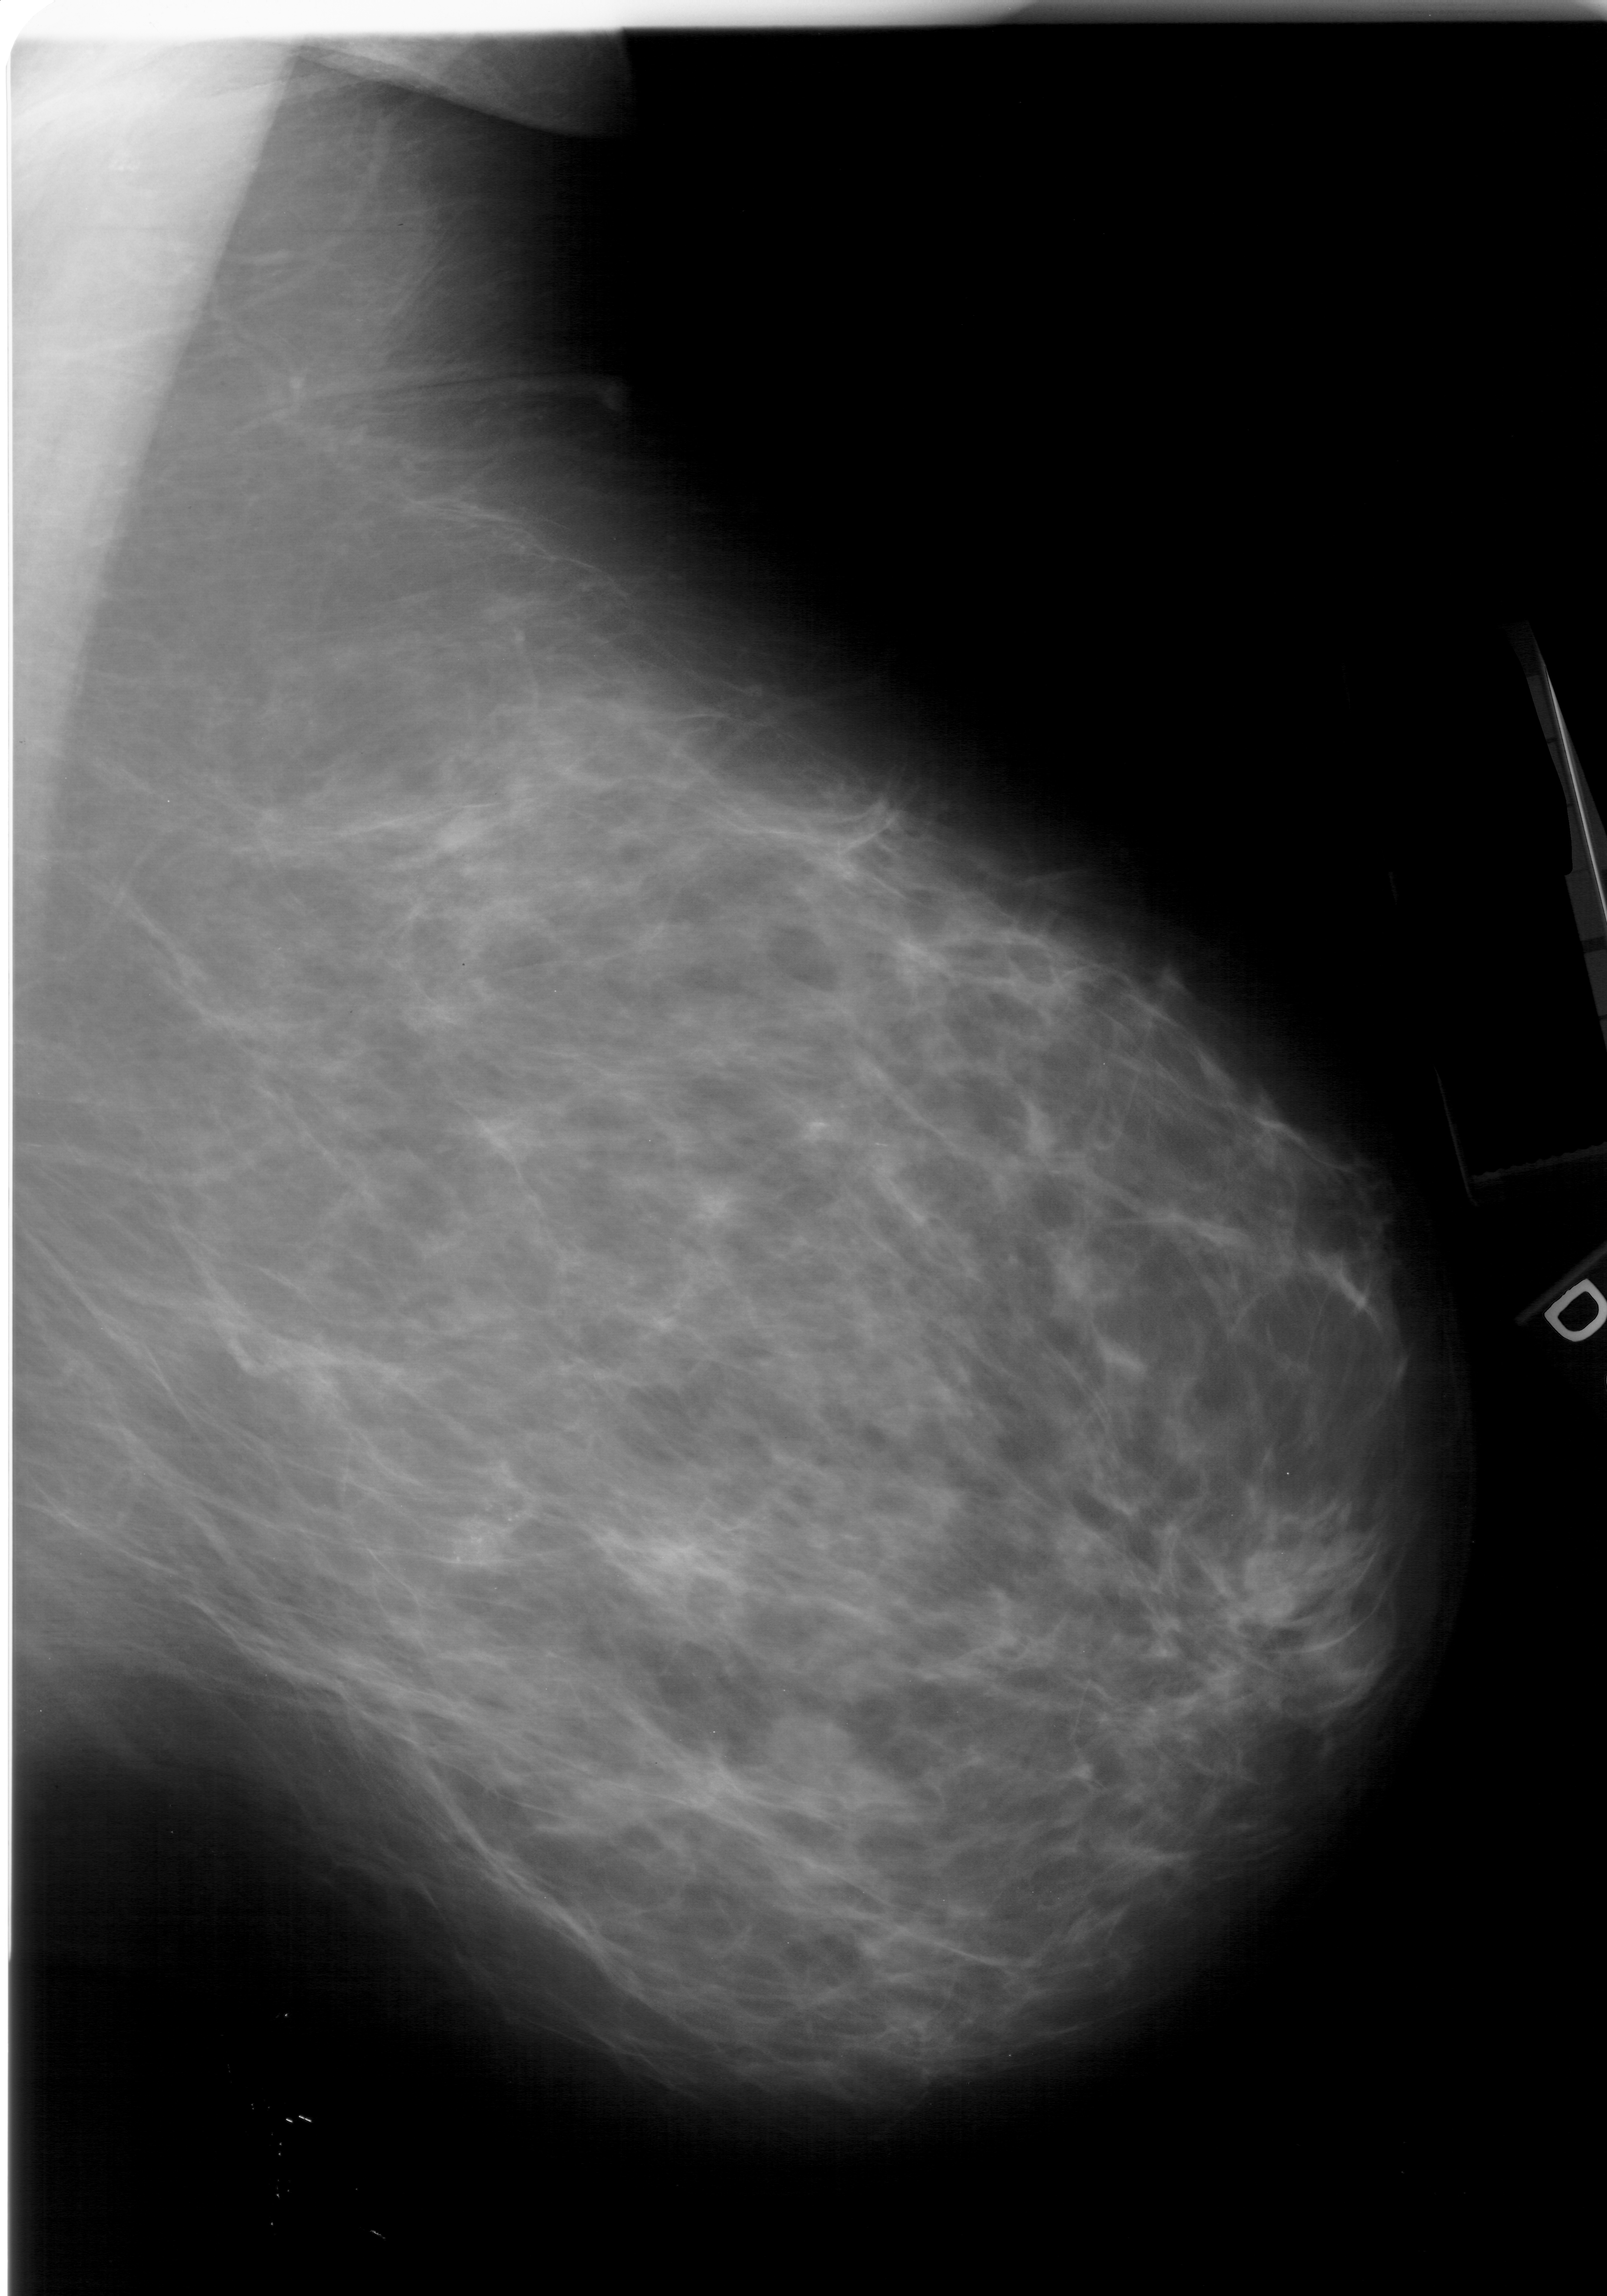
Mammogram (digitized film); right breast; mediolateral oblique (MLO) view; breast composition: almost entirely fatty (BI-RADS density category 1 of 4); 1607 × 2296 image matrix.
Expert-marked regions of interest on this image (one box per marked abnormality):
- calcifications, morphology pleomorphic, distribution linear; BI-RADS assessment category 4; subtlety rating 3 on a 1 (subtle) to 5 (obvious) scale; pathology result (as recorded, not read from the image): malignant: box from (x=447, y=1488) to (x=543, y=1589) px